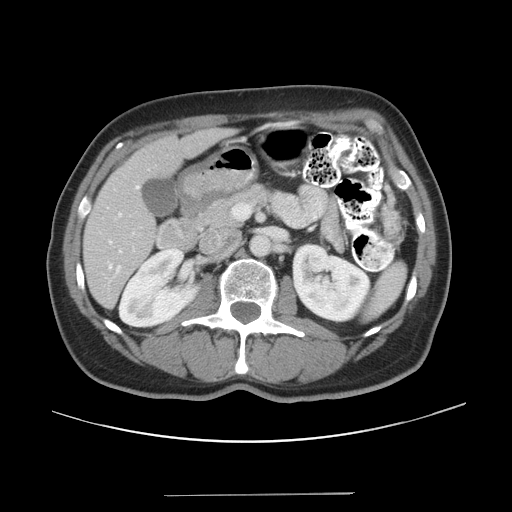
Contrast-enhanced abdominal CT, one axial slice; slice 17 of 43 in the series (ordered by position); reconstruction kernel STANDARD; intravenous contrast given; soft-tissue window (W 400 / L 40 HU); 512 × 512 image matrix. Male patient, age 65 years. Case-level facts recorded for this patient, not image findings: diagnosis: colorectal cancer liver metastases, imaged before liver resection; multiple liver metastases: no; largest metastasis: 3.8 cm.
Outlined on this slice (manually delineated by an expert):
- hepatic veins: bounding box <109,241,122,268> (left, top, right, bottom; pixels)
- liver: <84,130,227,306>
- planned liver remnant (the part of the liver to remain after resection): <84,130,227,306>